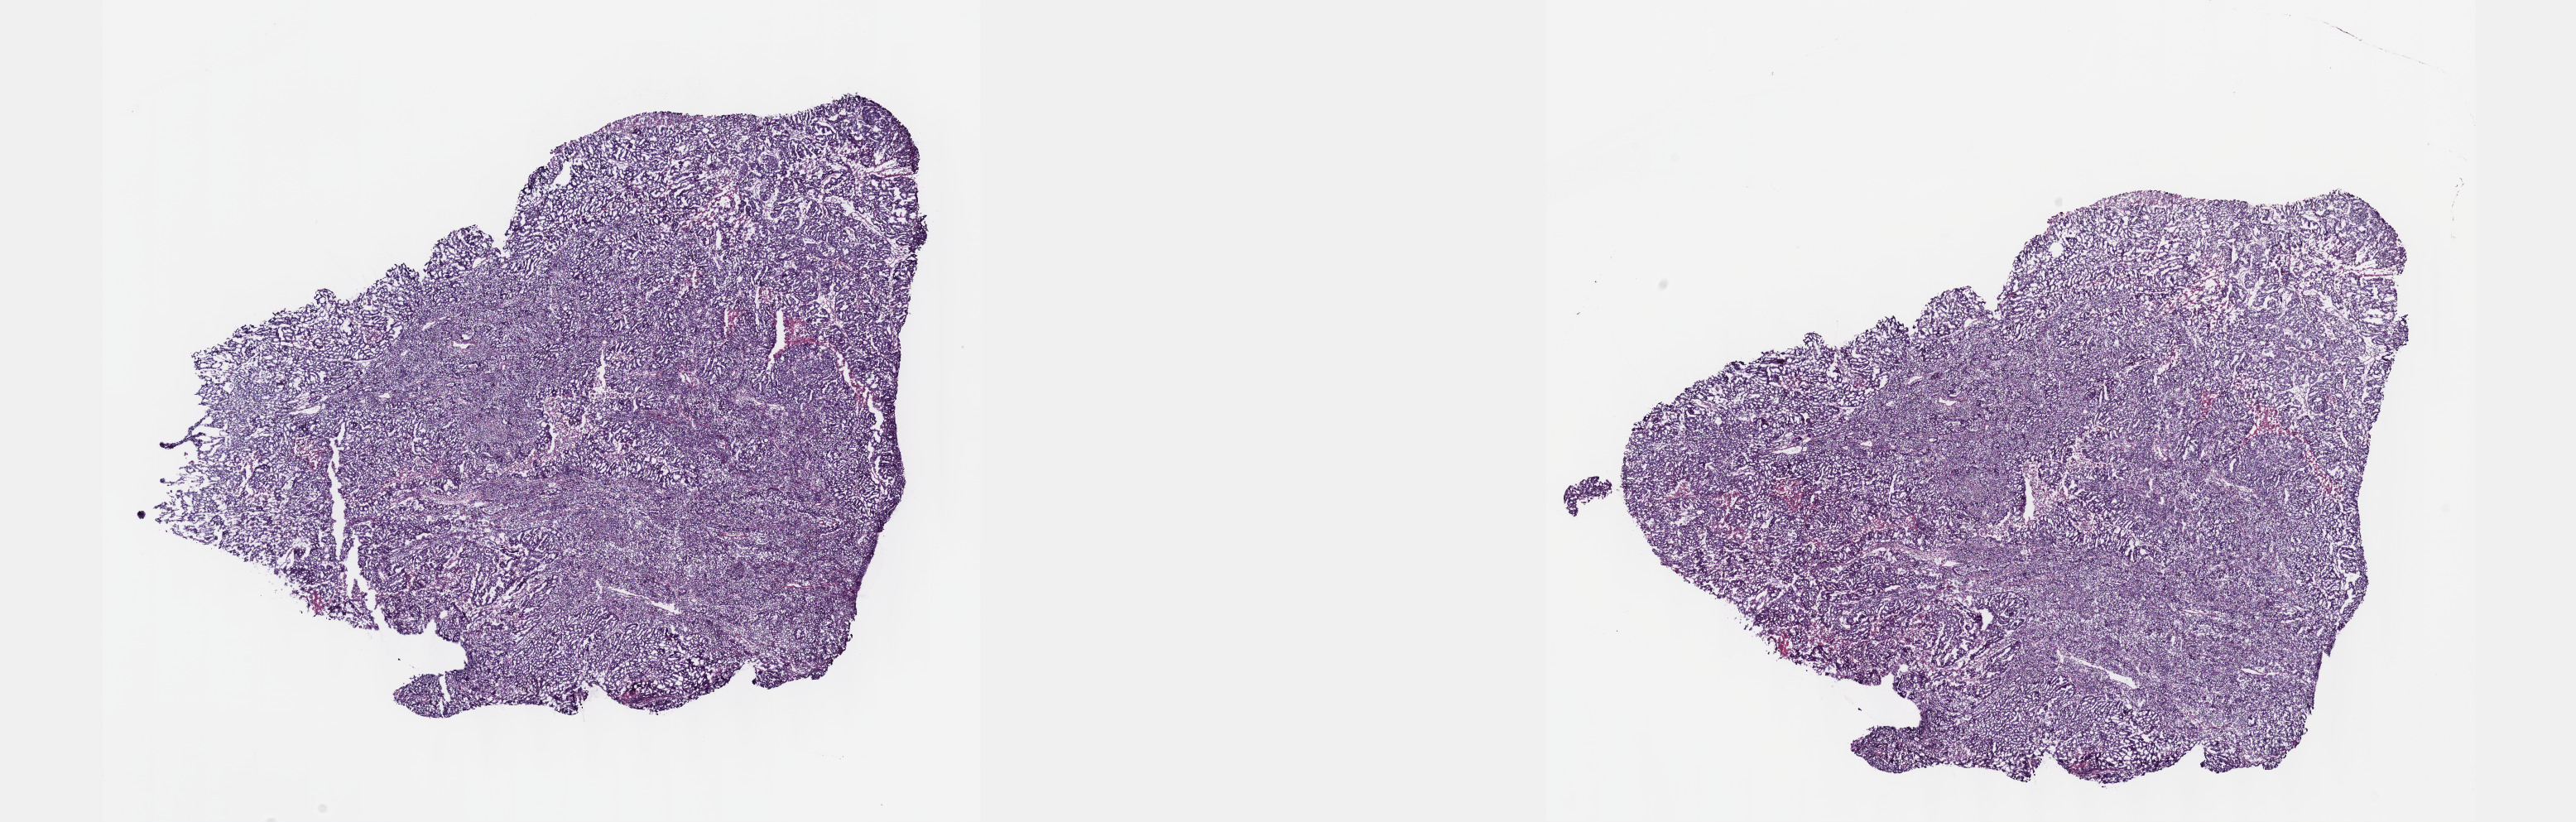
Whole-slide histology image, Hematoxylin and eosin (H&E) stained, shown as a low-resolution overview of the whole scanned area (about 25.1 x 8.0 mm, acquisition: 40x scan); frozen section; uterus, primary tumour sample. Patient: female, age at initial diagnosis 59 years. Histologic grade: G2 (moderately differentiated). Slide review estimates, as recorded: tumour cells 80%, tumour nuclei 80%, normal cells 0%, stromal cells 15%, necrosis 5%. Inflammatory infiltration, as recorded: lymphocyte infiltration 10%, monocyte infiltration 0%, neutrophil infiltration 0%.
FIGO stage: III. Diagnosis: Endometrioid adenocarcinoma, NOS.